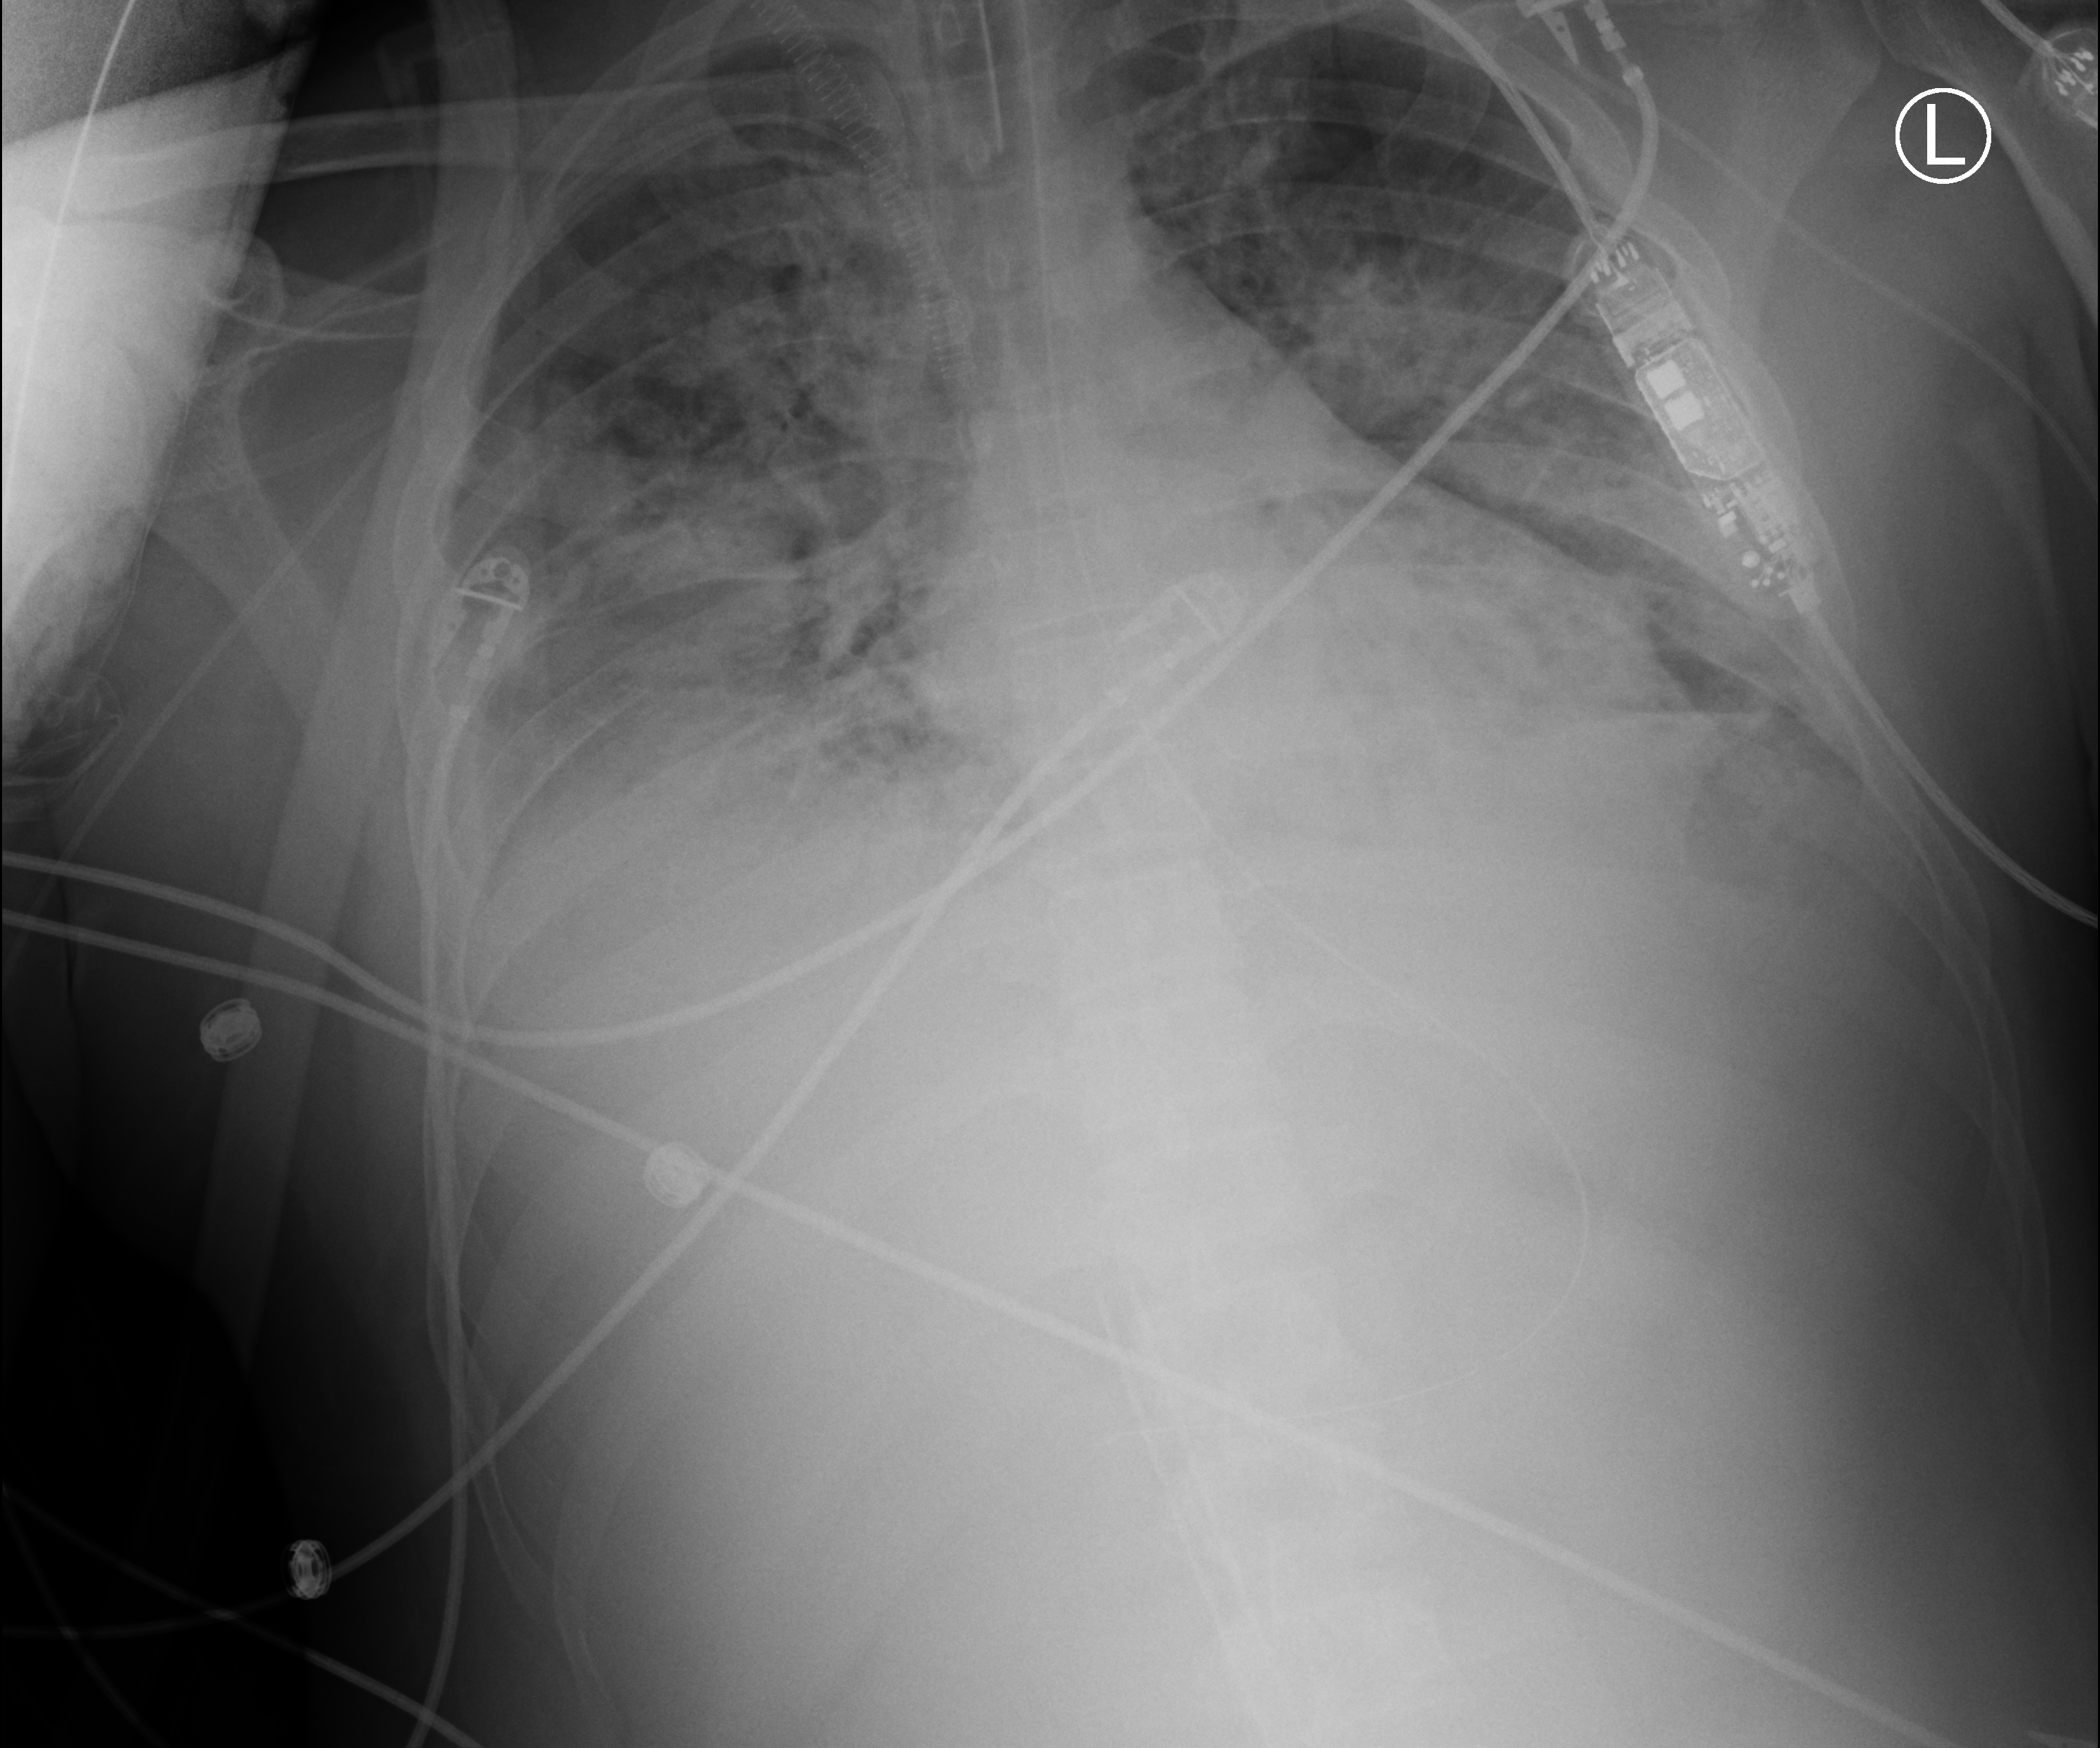
Bedside chest radiograph (computed radiography); anteroposterior (AP) projection. Adult patient hospitalised with COVID-19, age 18–59 years.
Hospital-stay facts (about this admission, not read from this image; timing relative to this image not recorded): mechanically ventilated during this hospital stay: yes.